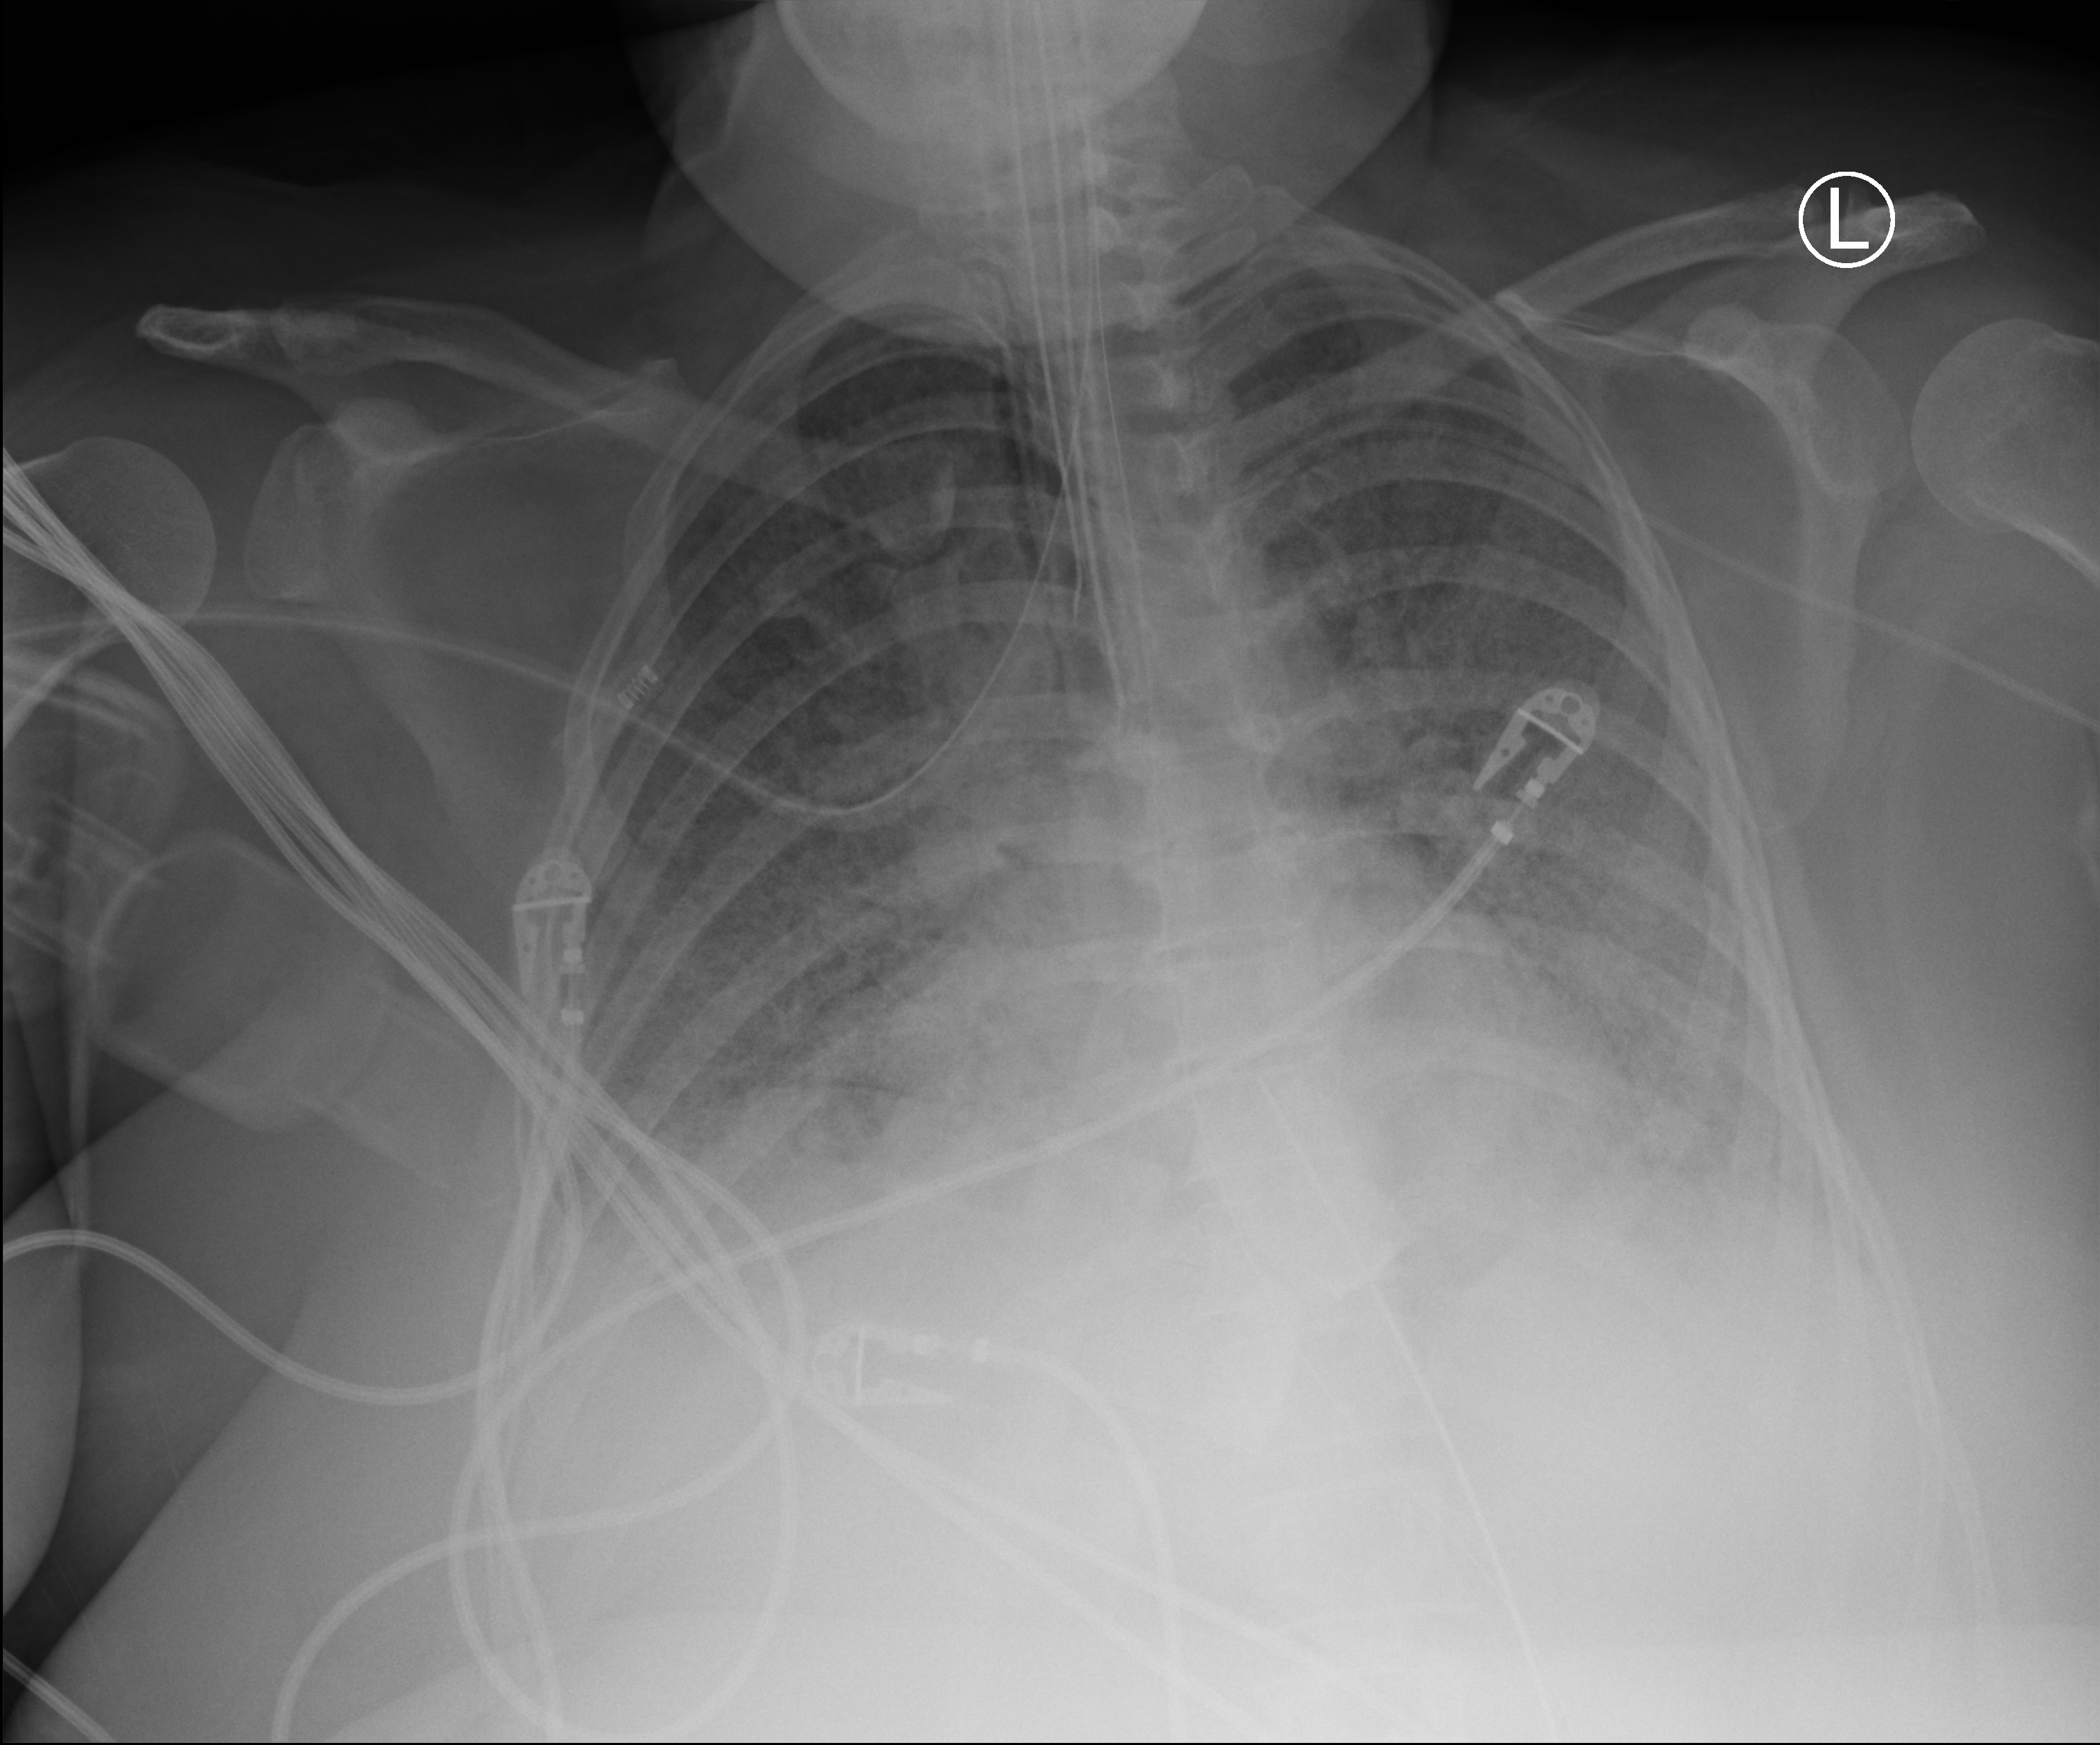
Portable chest radiograph. Patient hospitalised with COVID-19; female, aged 18–59 years.
From the hospital-stay record, not from the radiograph (when in the stay this image was taken is not recorded): smoking status (admission record): never; admitted to intensive care during this hospital stay: yes; mechanically ventilated during this hospital stay: yes.